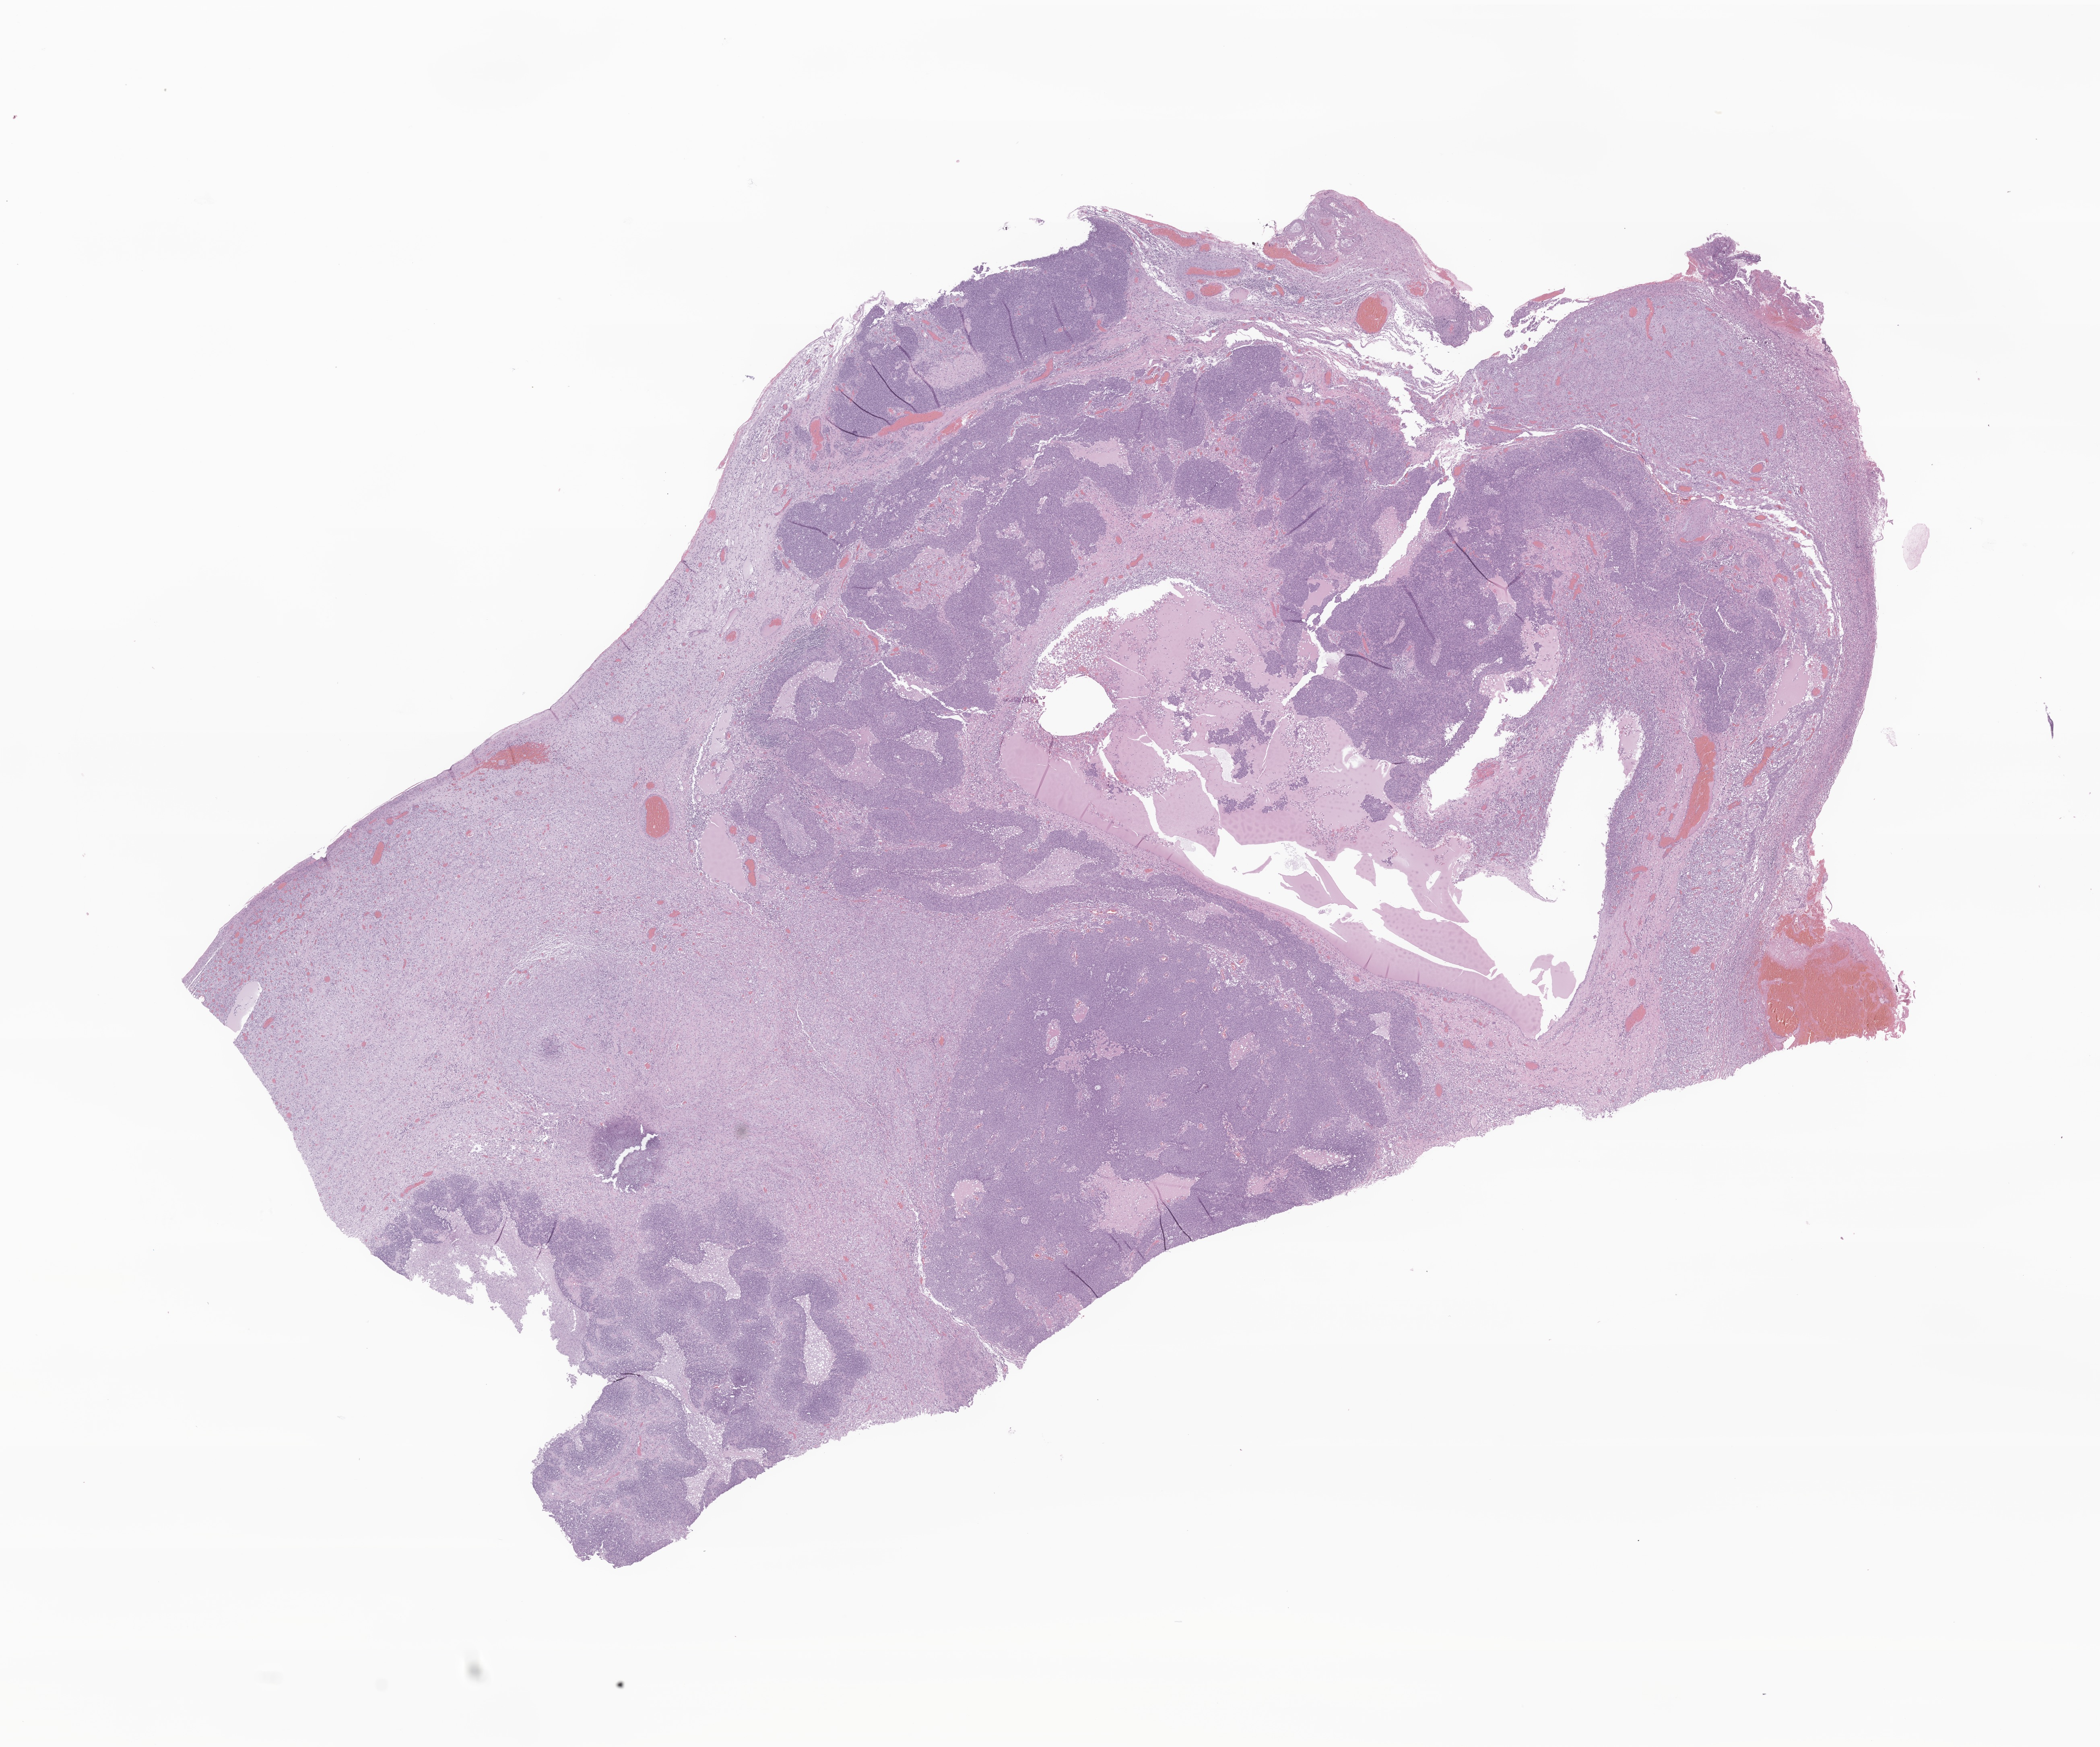
Whole-slide image, haematoxylin and eosin stain of tumor tissue from the cerebral meninges, low-resolution overview of the scanned area, about 22.0 x 18.3 mm; formalin-fixed, paraffin-embedded (FFPE) tissue. Patient male; age 119 months (9 years 11 months).
* diagnosis: Meningioma, malignant